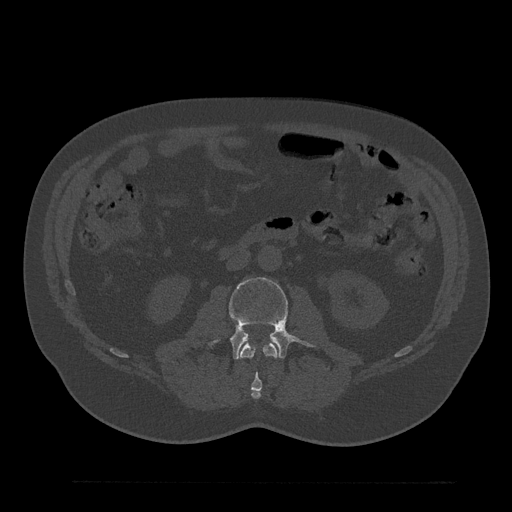
CT including the spine, one axial slice; position 58 of 797 along the scan axis; 120 kVp; bone window (W 1800 / L 400 HU); 0.5 mm slice thickness; 512 × 512 image matrix. Patient: male, 61 years. Case-level facts recorded for this patient, not image findings: primary cancer: prostate.
Annotated regions visible in this slice (semi-automatic segmentation, software-assisted and operator-edited):
- L2 vertebra: bounding box [x1, y1, x2, y2] px = [239, 342, 278, 399]
- L3 vertebra: [228, 277, 311, 359]